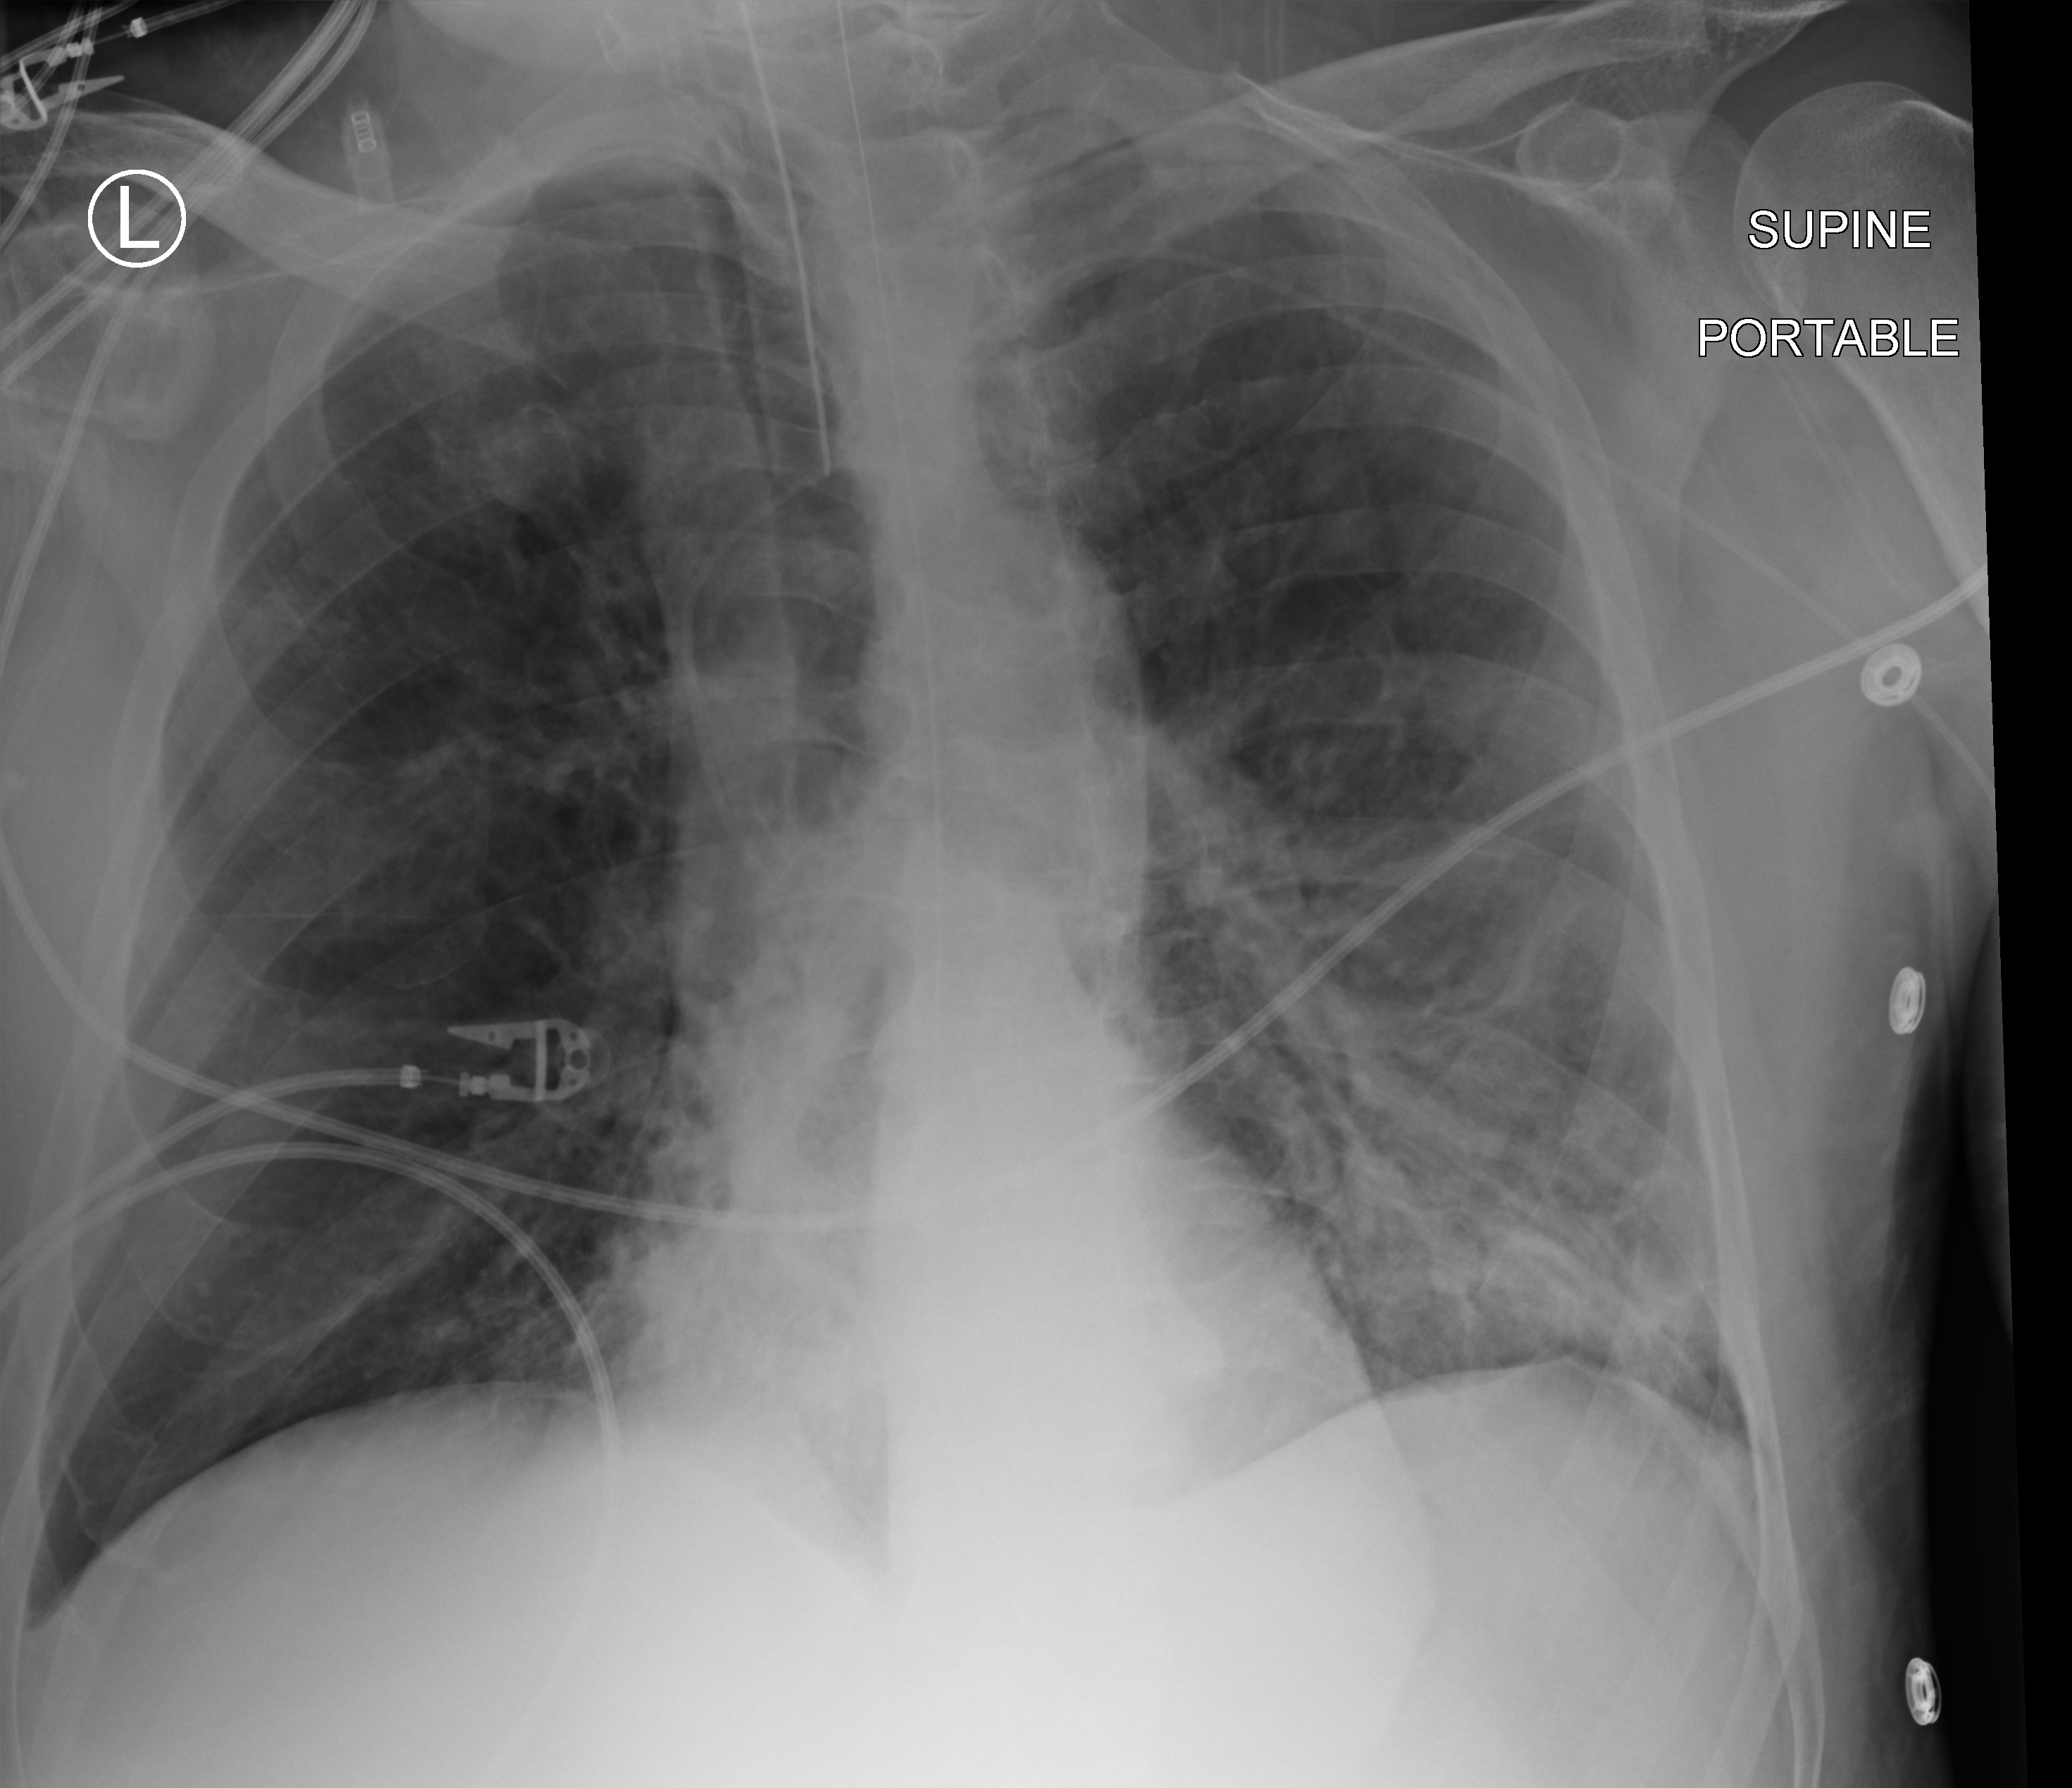
Bedside chest radiograph (computed radiography); anteroposterior (AP) projection. Patient hospitalised with COVID-19; male, aged 60–74 years.
From the hospital-stay record, not from the radiograph (when in the stay this image was taken is not recorded): admitted to intensive care during this hospital stay: yes; length of hospital stay: 35 days.